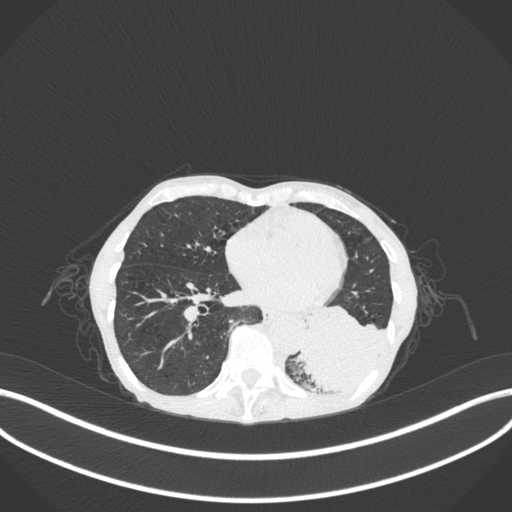
Chest CT, one axial slice. Position 94 of 347 along the scan axis. Reconstruction kernel B31f. Lung window (W 1500 / L -600 HU). 1 mm slice thickness. 512 × 512 image matrix, field of view 400 × 400 mm. Female patient, age 70 years. Case-level facts recorded for this patient, not image findings: clinical TNM (as recorded): T3 N0 M0.
Outlined on this slice (bounding box drawn by a radiologist):
- lung tumour (recorded histology: small cell carcinoma): bounding box (x1, y1, x2, y2) in pixels: (297, 295, 394, 396)